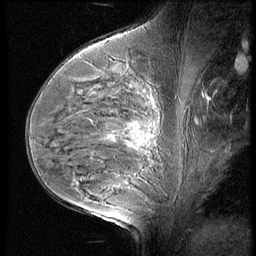
Breast MRI (dynamic contrast-enhanced), one sagittal slice. Position 36 of 60 along the scan axis. 3 images stored at this slice position (order not interpretable as contrast timing). 1.5 T. TE 4.2 ms, TR 9 ms. 2.5 mm slice thickness. 256 × 256 image matrix, field of view 180 × 180 mm. Patient: female, 35 years. Case-level facts recorded for this patient, not image findings: setting: breast cancer imaged before/during neoadjuvant chemotherapy; receptor status: HR-positive, HER2-negative.
Outlined on this slice (semi-automatic segmentation, software-assisted and operator-edited):
- analysis volume of interest (the breast-tissue region the enhancement analysis was run in; not a lesion): box from (x=56, y=58) to (x=176, y=202) px
- tumour enhancement mask (voxels above the 140 % enhancement threshold inside the analysis volume of interest): (x=125, y=142)–(x=143, y=148)